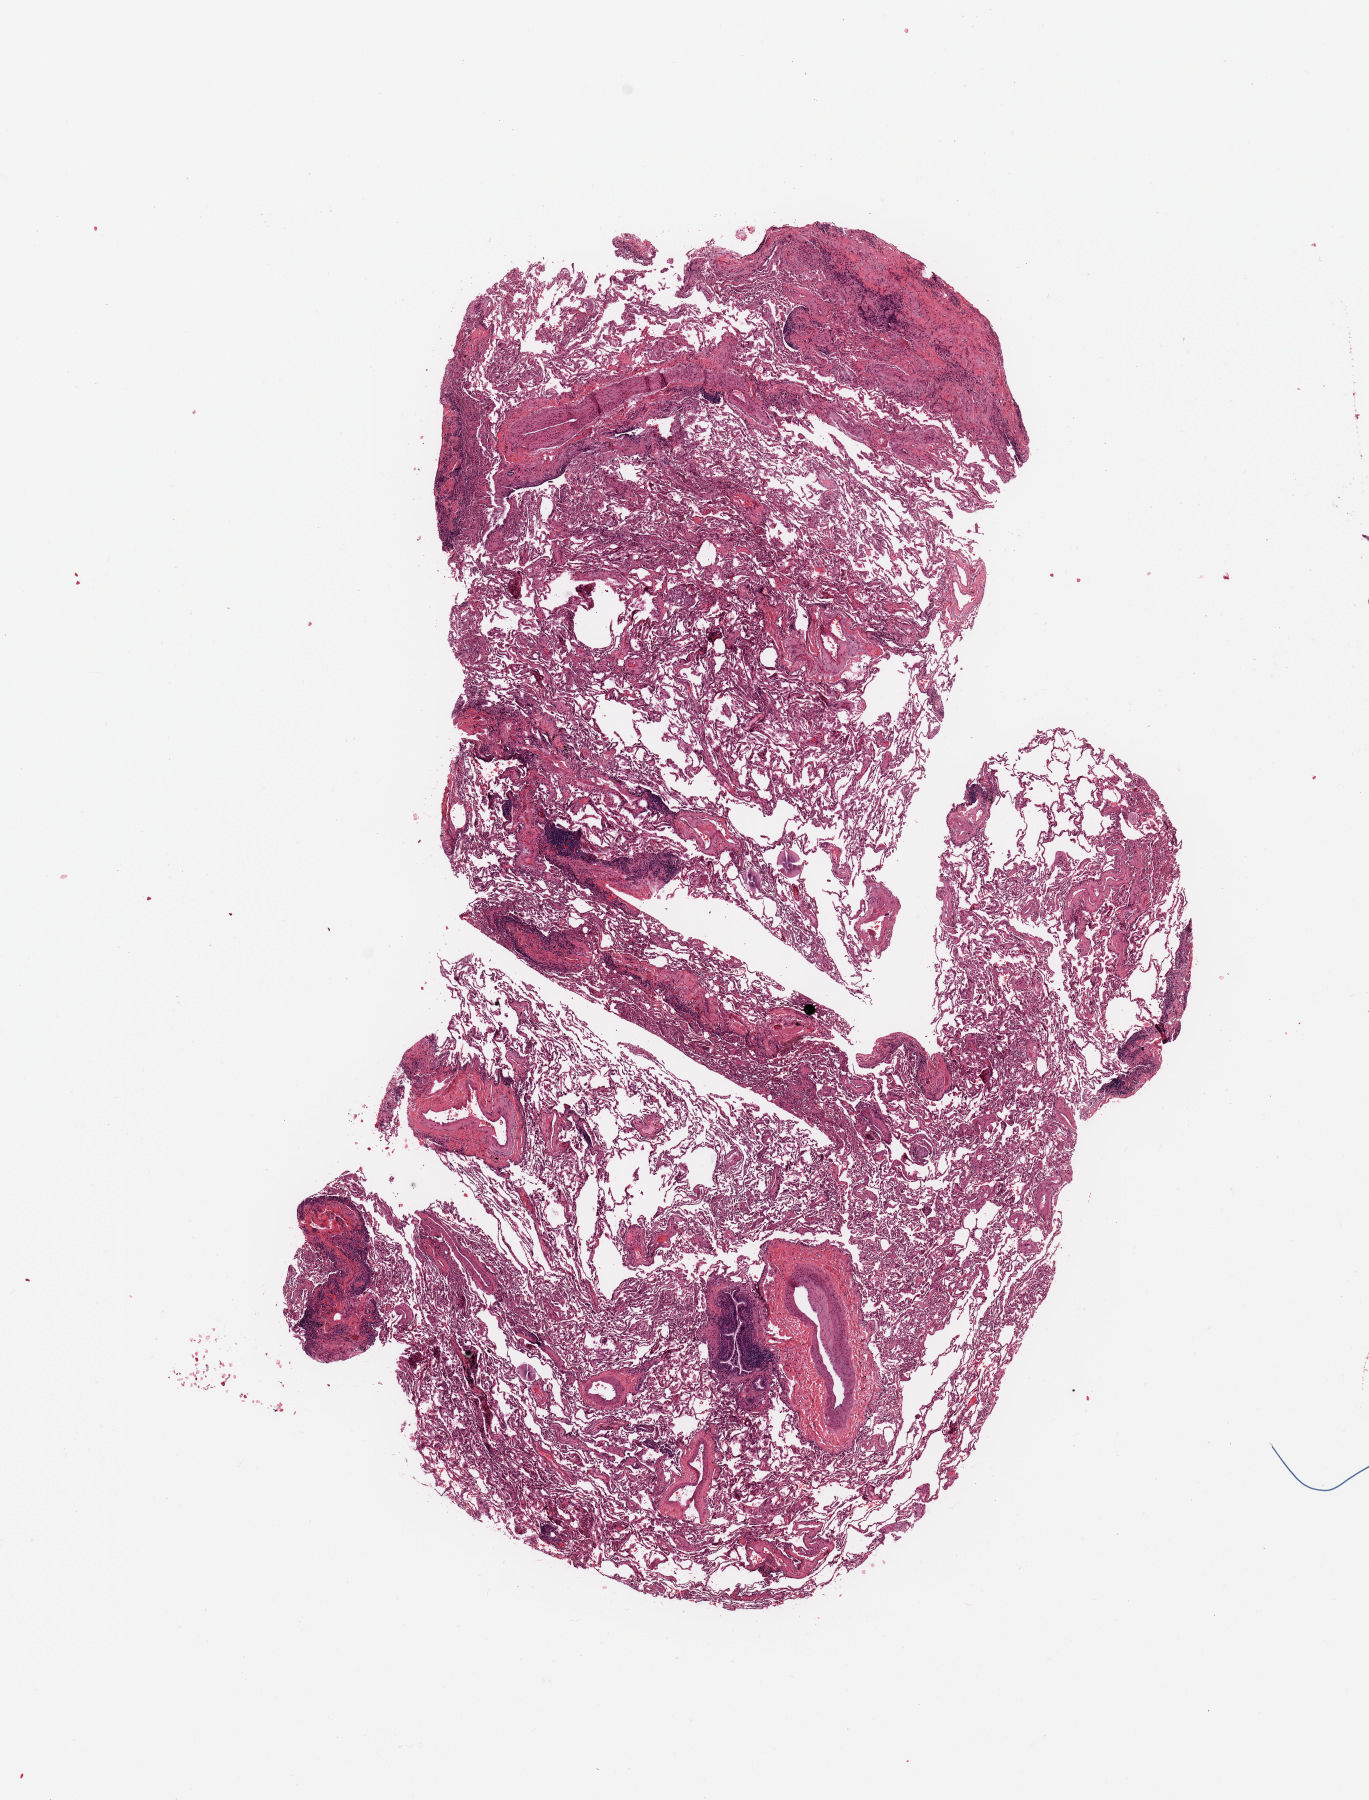
H&E whole-slide image, whole scanned area (about 10.8 x 14.2 mm) shown as a low-resolution overview; normal (non-tumour) tissue sample, sampled site: lung. Patient: male, age 88 years.
This section: normal (non-tumour) tissue from the same patient. Patient diagnosis: Squamous cell carcinoma, NOS.